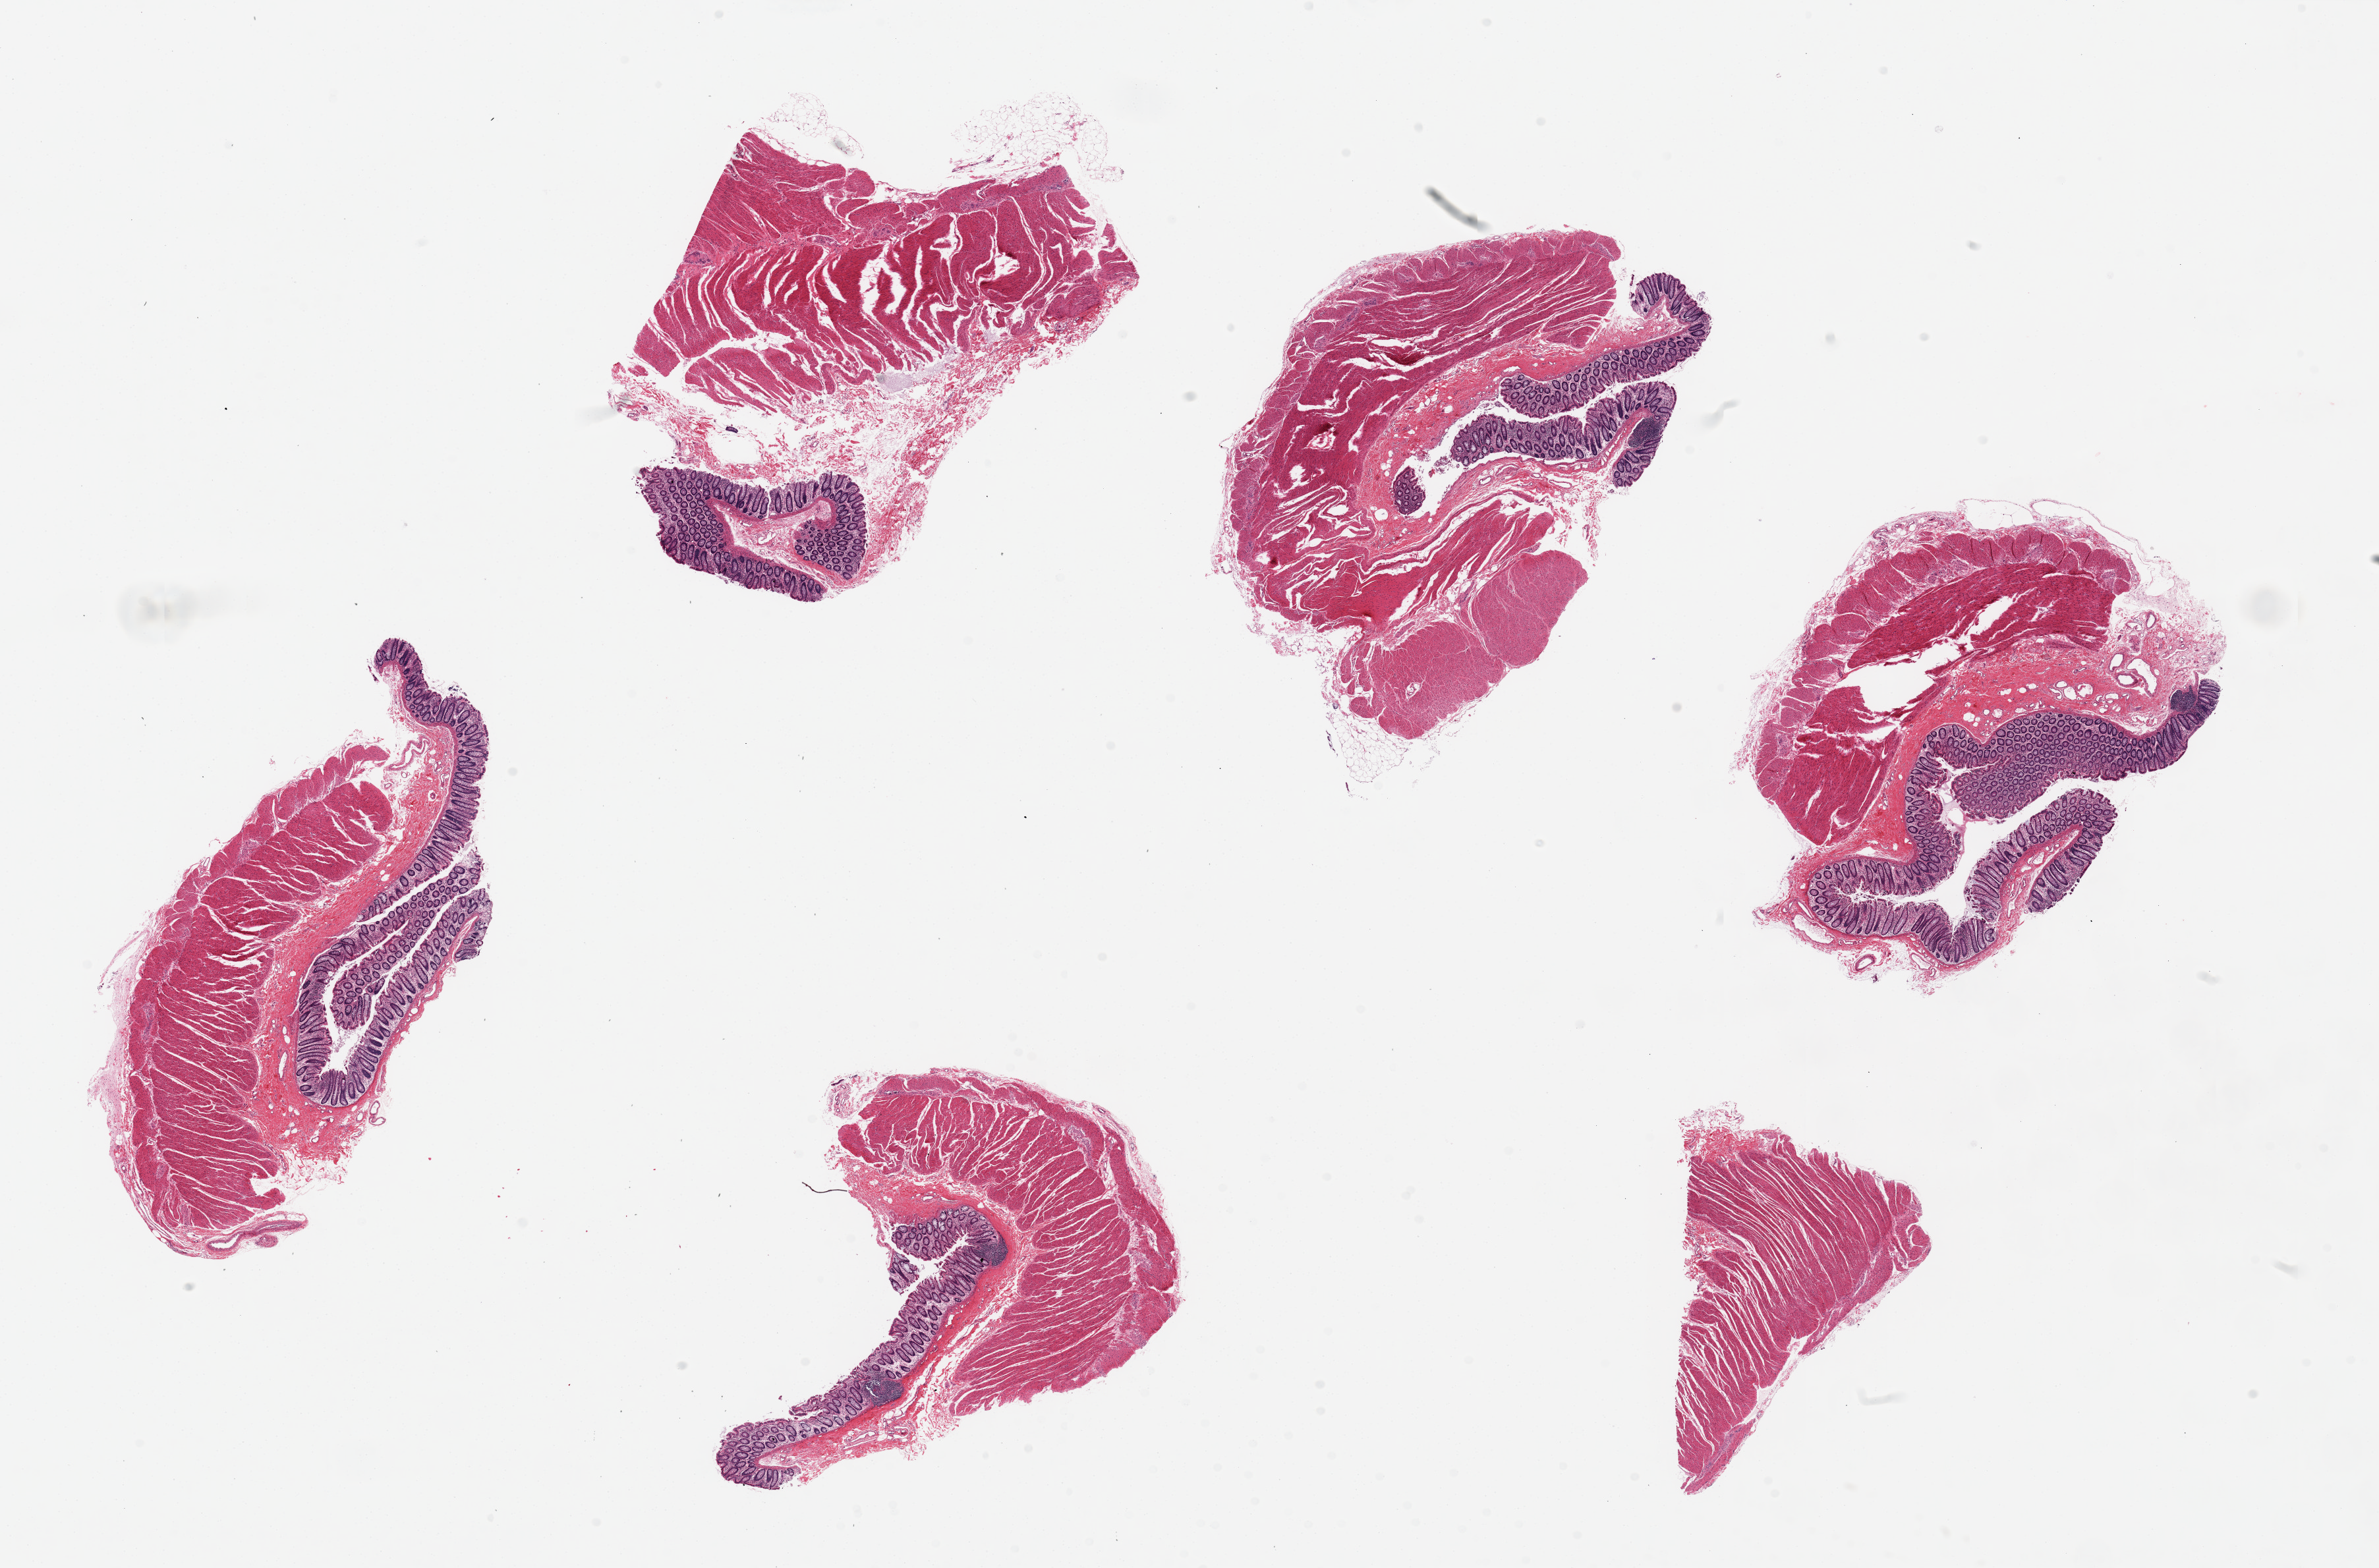
Whole-slide image, H&E stain, shown as a low-resolution overview of the whole scanned area (about 28.5 x 18.8 mm, acquisition: 20x scan); PAXgene-fixed, paraffin-embedded tissue; target tissue: transverse colon; donor tissue sample. Donor sex: female.
* reviewer comment on this tissue sample: 6 pieces ~6x5mm. Muscosa <~ 10% of thickness